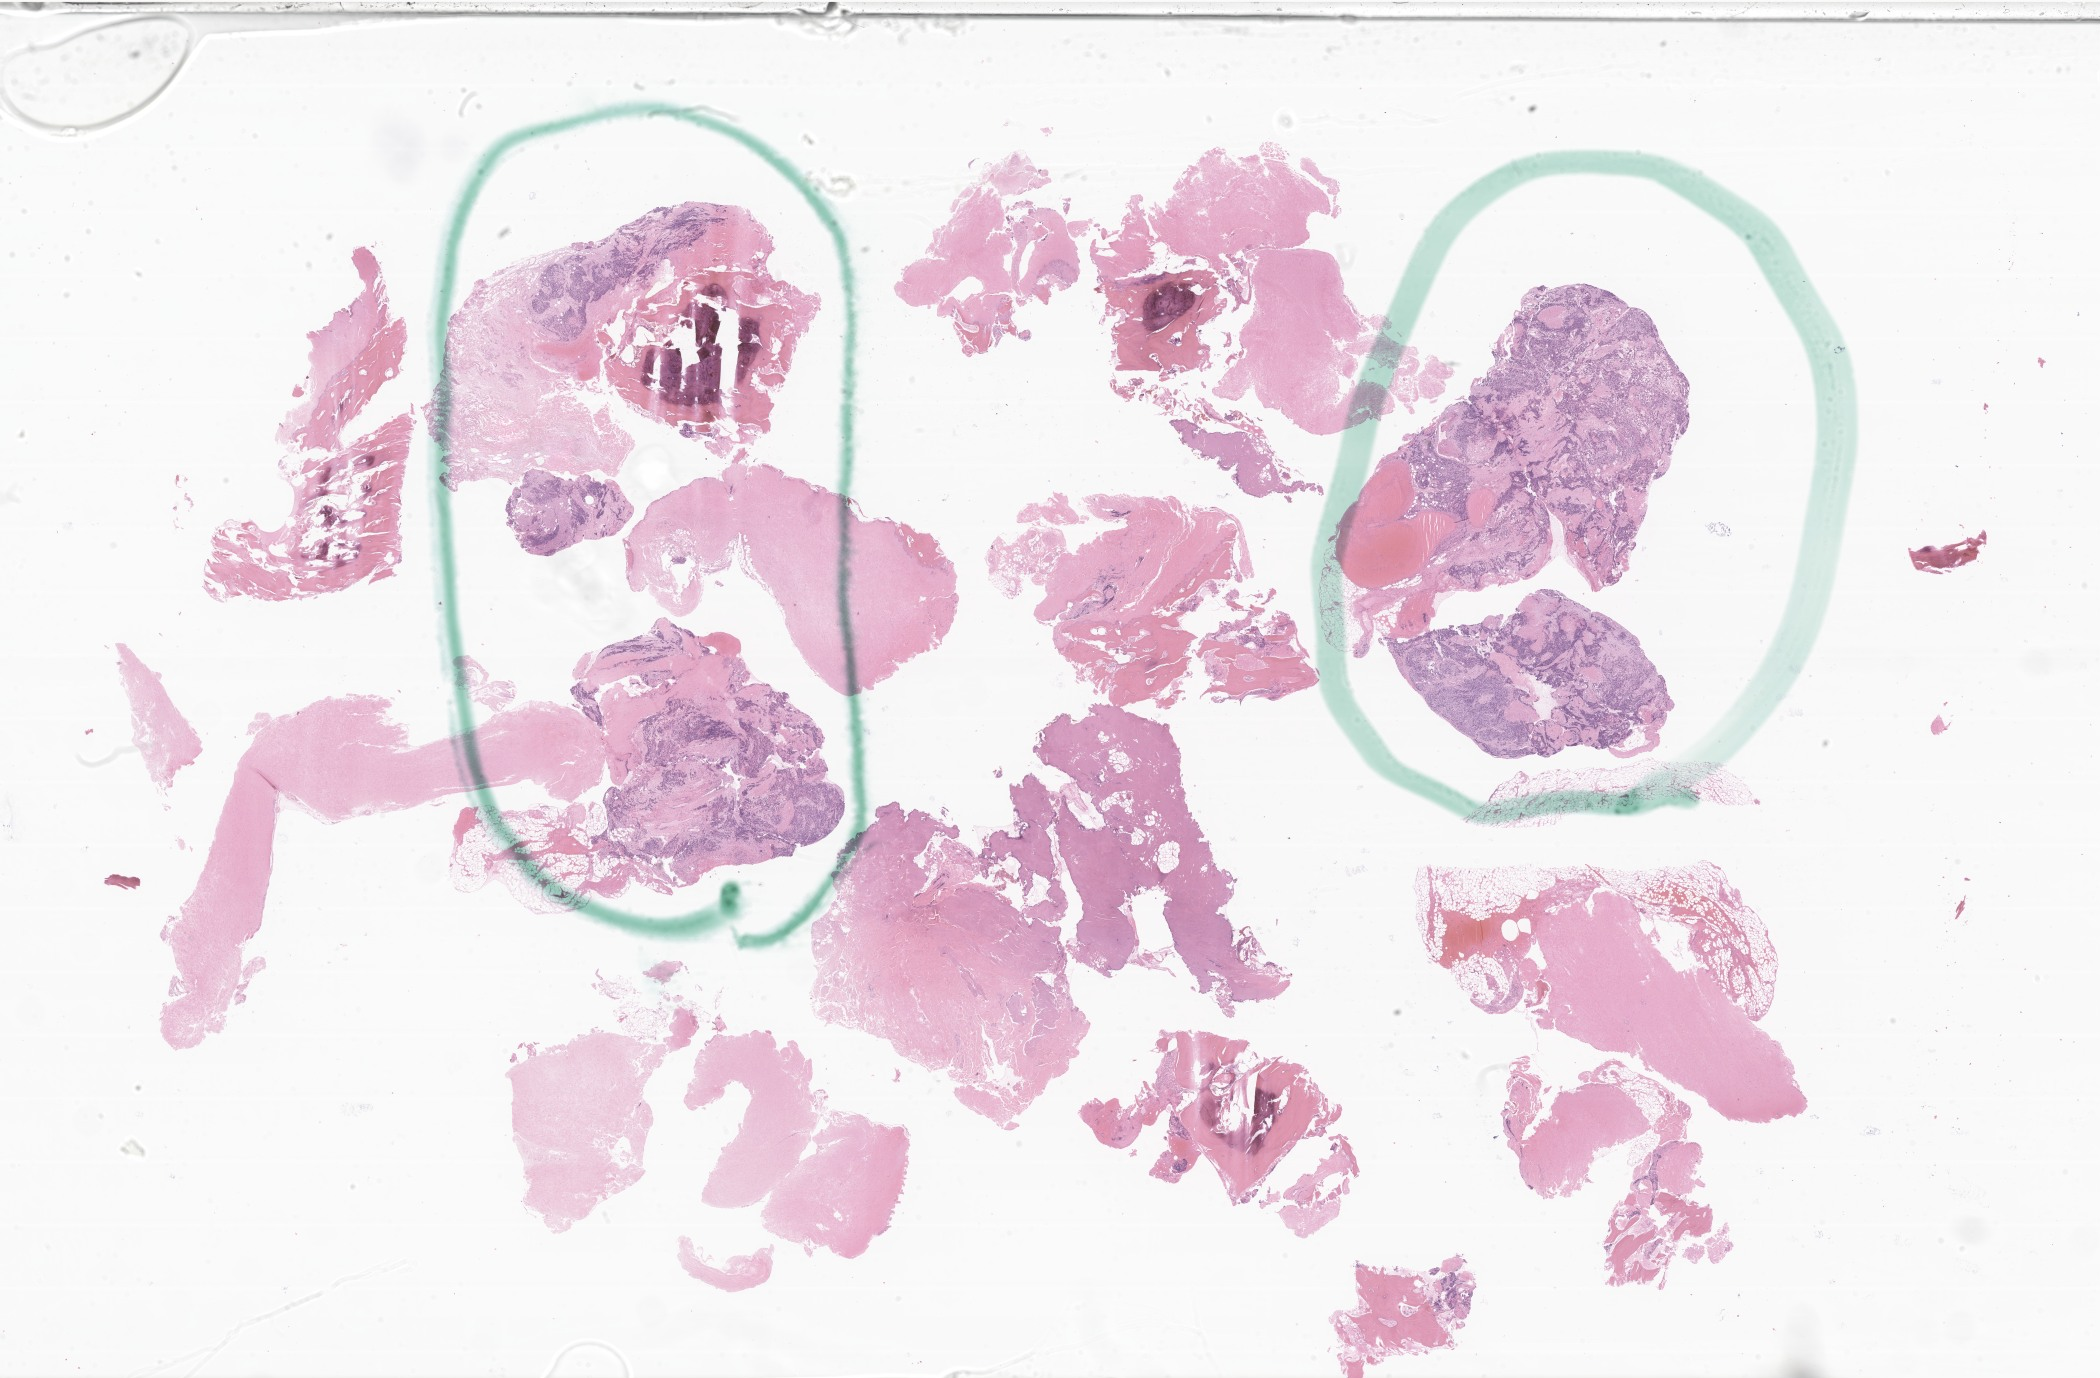
Digitized H&E-stained section of tumor tissue, whole scanned area (about 35.4 x 23.2 mm) shown as a low-resolution overview; FFPE section. Patient female; age 244 months (20 years 4 months).
Recorded diagnosis: Alveolar rhabdomyosarcoma.